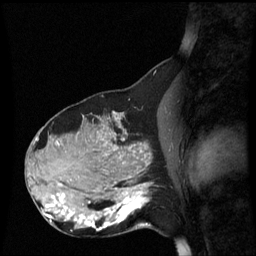
Breast MRI (dynamic contrast-enhanced), one sagittal slice; slice 28 of 60 in the series (ordered by position); dynamic contrast-enhanced series, image 2 of 3 at this slice position (ordered by acquisition); 1.5 T; TE 4.2 ms, TR 8.9 ms; 2.2 mm slice thickness; 256 × 256 image matrix, field of view 220 × 220 mm. Female patient, age 31 years. From the clinical record (not read from this slice): setting: breast cancer imaged before/during neoadjuvant chemotherapy; receptor status: HR-positive, HER2-negative.
Outlined on this slice (semi-automatic segmentation, software-assisted and operator-edited):
- analysis volume of interest (the breast-tissue region the enhancement analysis was run in; not a lesion): bounding box [x1, y1, x2, y2] px = [90, 180, 152, 235]
- tumour enhancement mask (voxels above the 70 % enhancement threshold inside the analysis volume of interest): [90, 184, 149, 231]